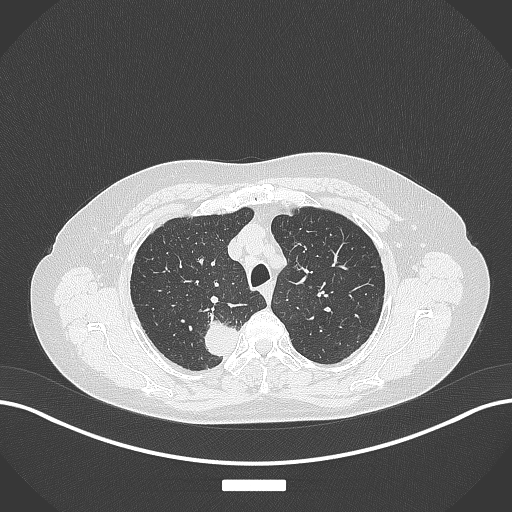
Chest CT, one axial slice. Slice 309 of 357 in the series (ordered by position). Reconstruction kernel B70f. Lung window (W 1500 / L -600 HU). 512 × 512 image matrix, field of view 400 × 400 mm. Patient: female, 62 years. Case-level facts recorded for this patient, not image findings: clinical TNM (as recorded): T1c N1 M0.
Annotated regions visible in this slice (bounding box drawn by a radiologist):
- lung tumour (recorded histology: squamous cell carcinoma): bounding box <201,310,240,363> (left, top, right, bottom; pixels)